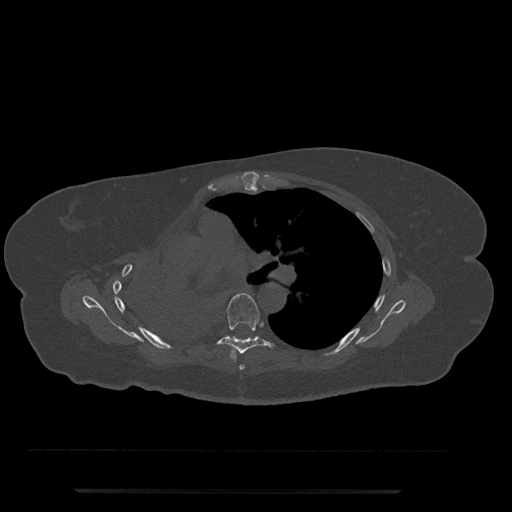
CT including the spine, one axial slice. Slice 497 of 797 in the series (ordered by position). Reconstruction kernel Br40s/3. Bone window (W 1800 / L 400 HU). 0.5 mm slice thickness. 512 × 512 image matrix, field of view 440 × 440 mm. Patient: female, 51 years. Case-level facts recorded for this patient, not image findings: primary cancer: neuro.
Annotated regions visible in this slice (semi-automatic segmentation, software-assisted and operator-edited):
- T5 vertebra: bounding box [x1, y1, x2, y2] px = [239, 364, 245, 370]
- T6 vertebra: [213, 293, 277, 360]